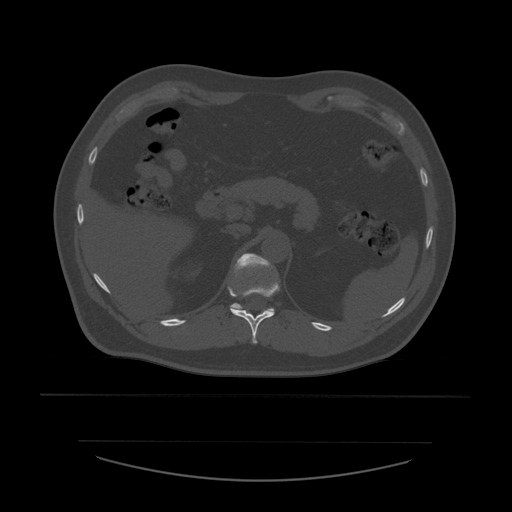
CT including the spine, one axial slice; position 267 of 532 along the scan axis; reconstruction kernel STANDARD; 120 kVp; bone window (W 1800 / L 400 HU); 1.25 mm slice thickness; 512 × 512 image matrix, field of view 441 × 441 mm. Patient age 44 years. Case-level facts recorded for this patient, not image findings: primary cancer: soft tissue sarcoma.
Structures marked on this image (semi-automatic segmentation, software-assisted and operator-edited):
- T11 vertebra: bounding box (x1, y1, x2, y2) in pixels: (231, 280, 280, 344)
- T12 vertebra: (228, 254, 274, 311)